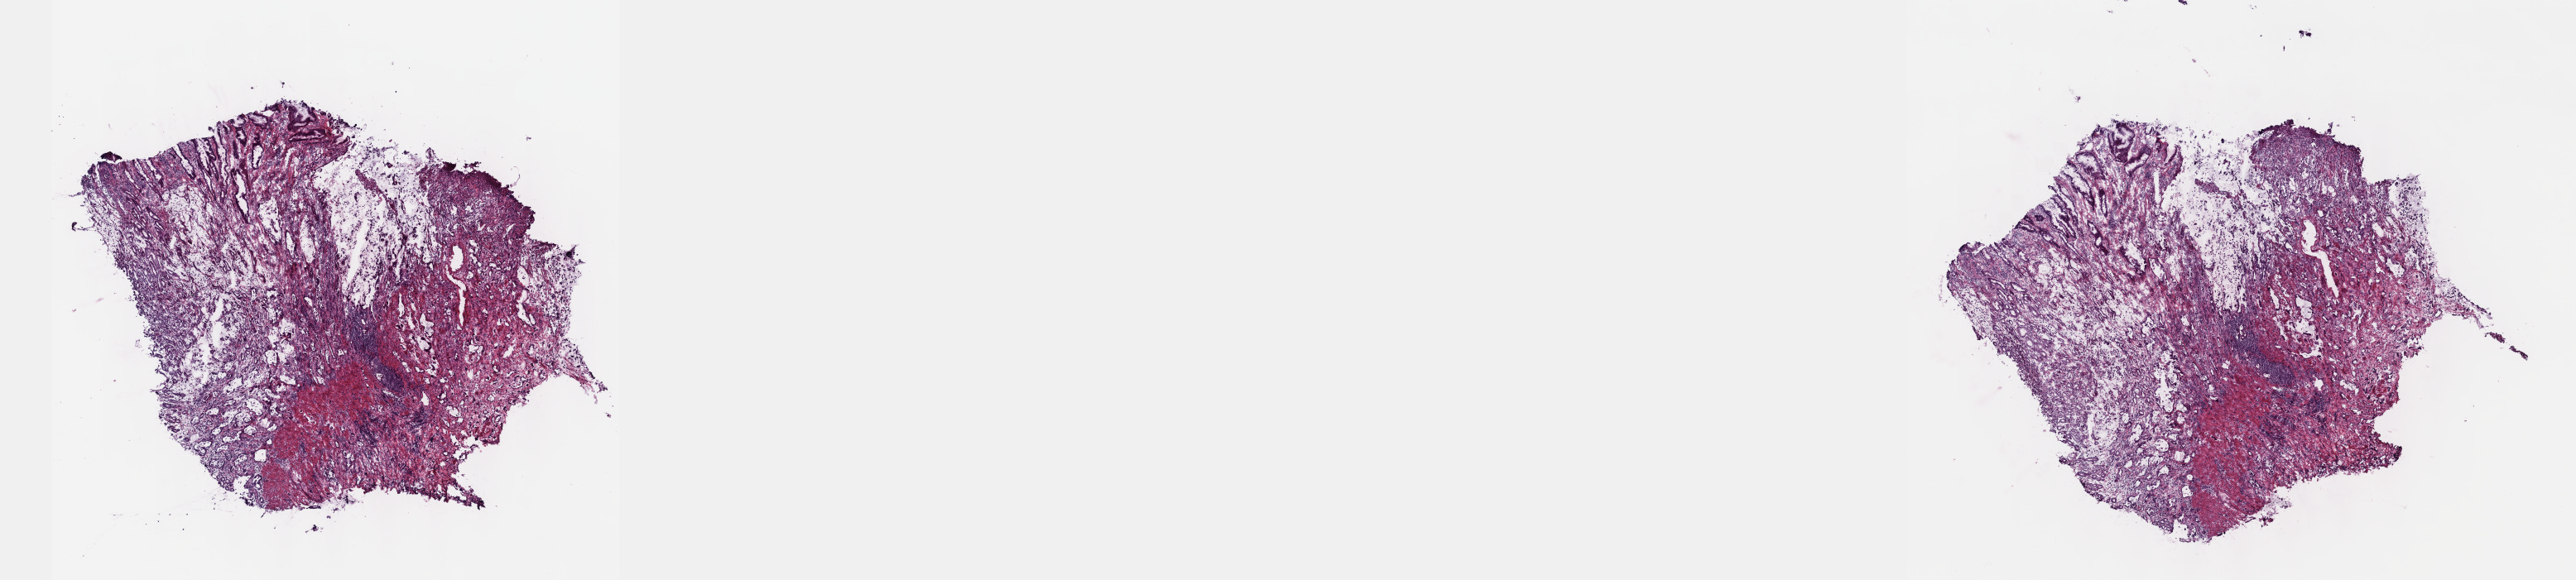
Digitized H&E tissue section (whole slide) — low-resolution overview of the scanned area, about 25.1 x 5.7 mm; frozen section; sample: primary tumour, stomach. Male patient; age at initial diagnosis 46 years. Histologic grade: G3 (poorly differentiated). Pathologist review of this section (percent, as recorded): tumour cells 90%, tumour nuclei 70%, normal cells 10%, stromal cells 0%, necrosis 0%. Inflammatory infiltration, as recorded: lymphocyte infiltration 5%, monocyte infiltration 0%, neutrophil infiltration 0%.
* pathologic diagnosis: Carcinoma, diffuse type (cardia, NOS)
* AJCC pathologic stage: IIIA (6th edition)
* TNM: T3 N1 M0